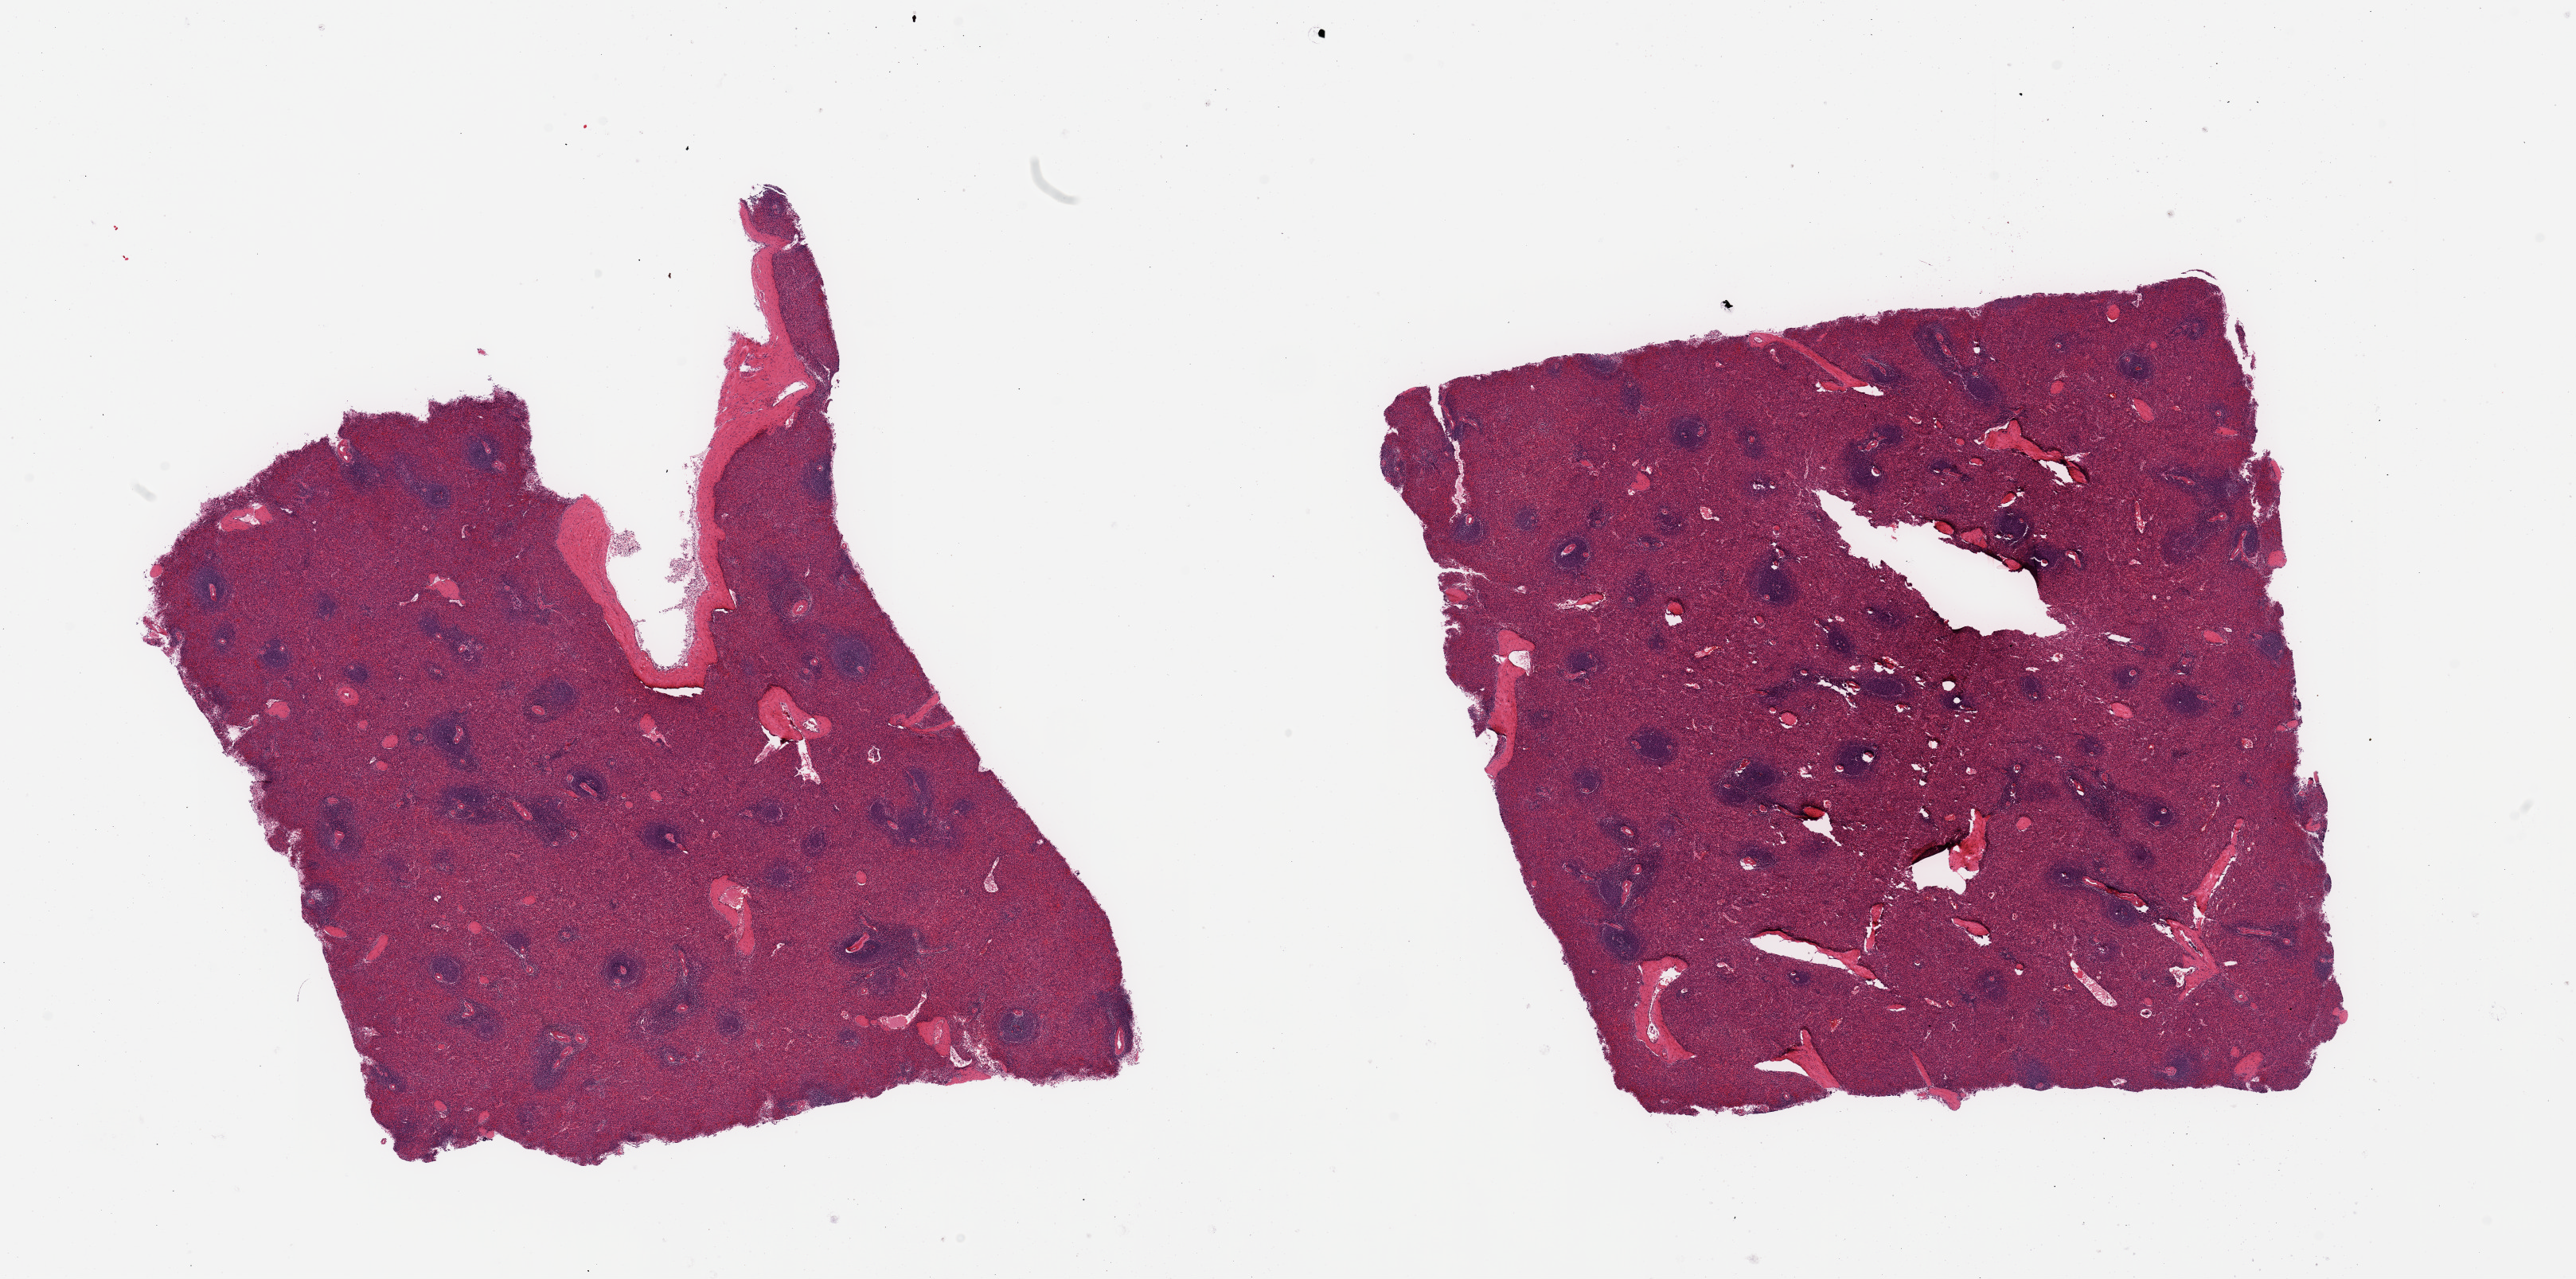
Haematoxylin and eosin whole-slide image, brightfield — shown as a low-resolution overview of the whole scanned area (about 25.6 x 12.7 mm); PAXgene-fixed, paraffin-embedded tissue; sampled site (target tissue): spleen; tissue donor sample.
* review note (as recorded): 2 pieces; slight congestion